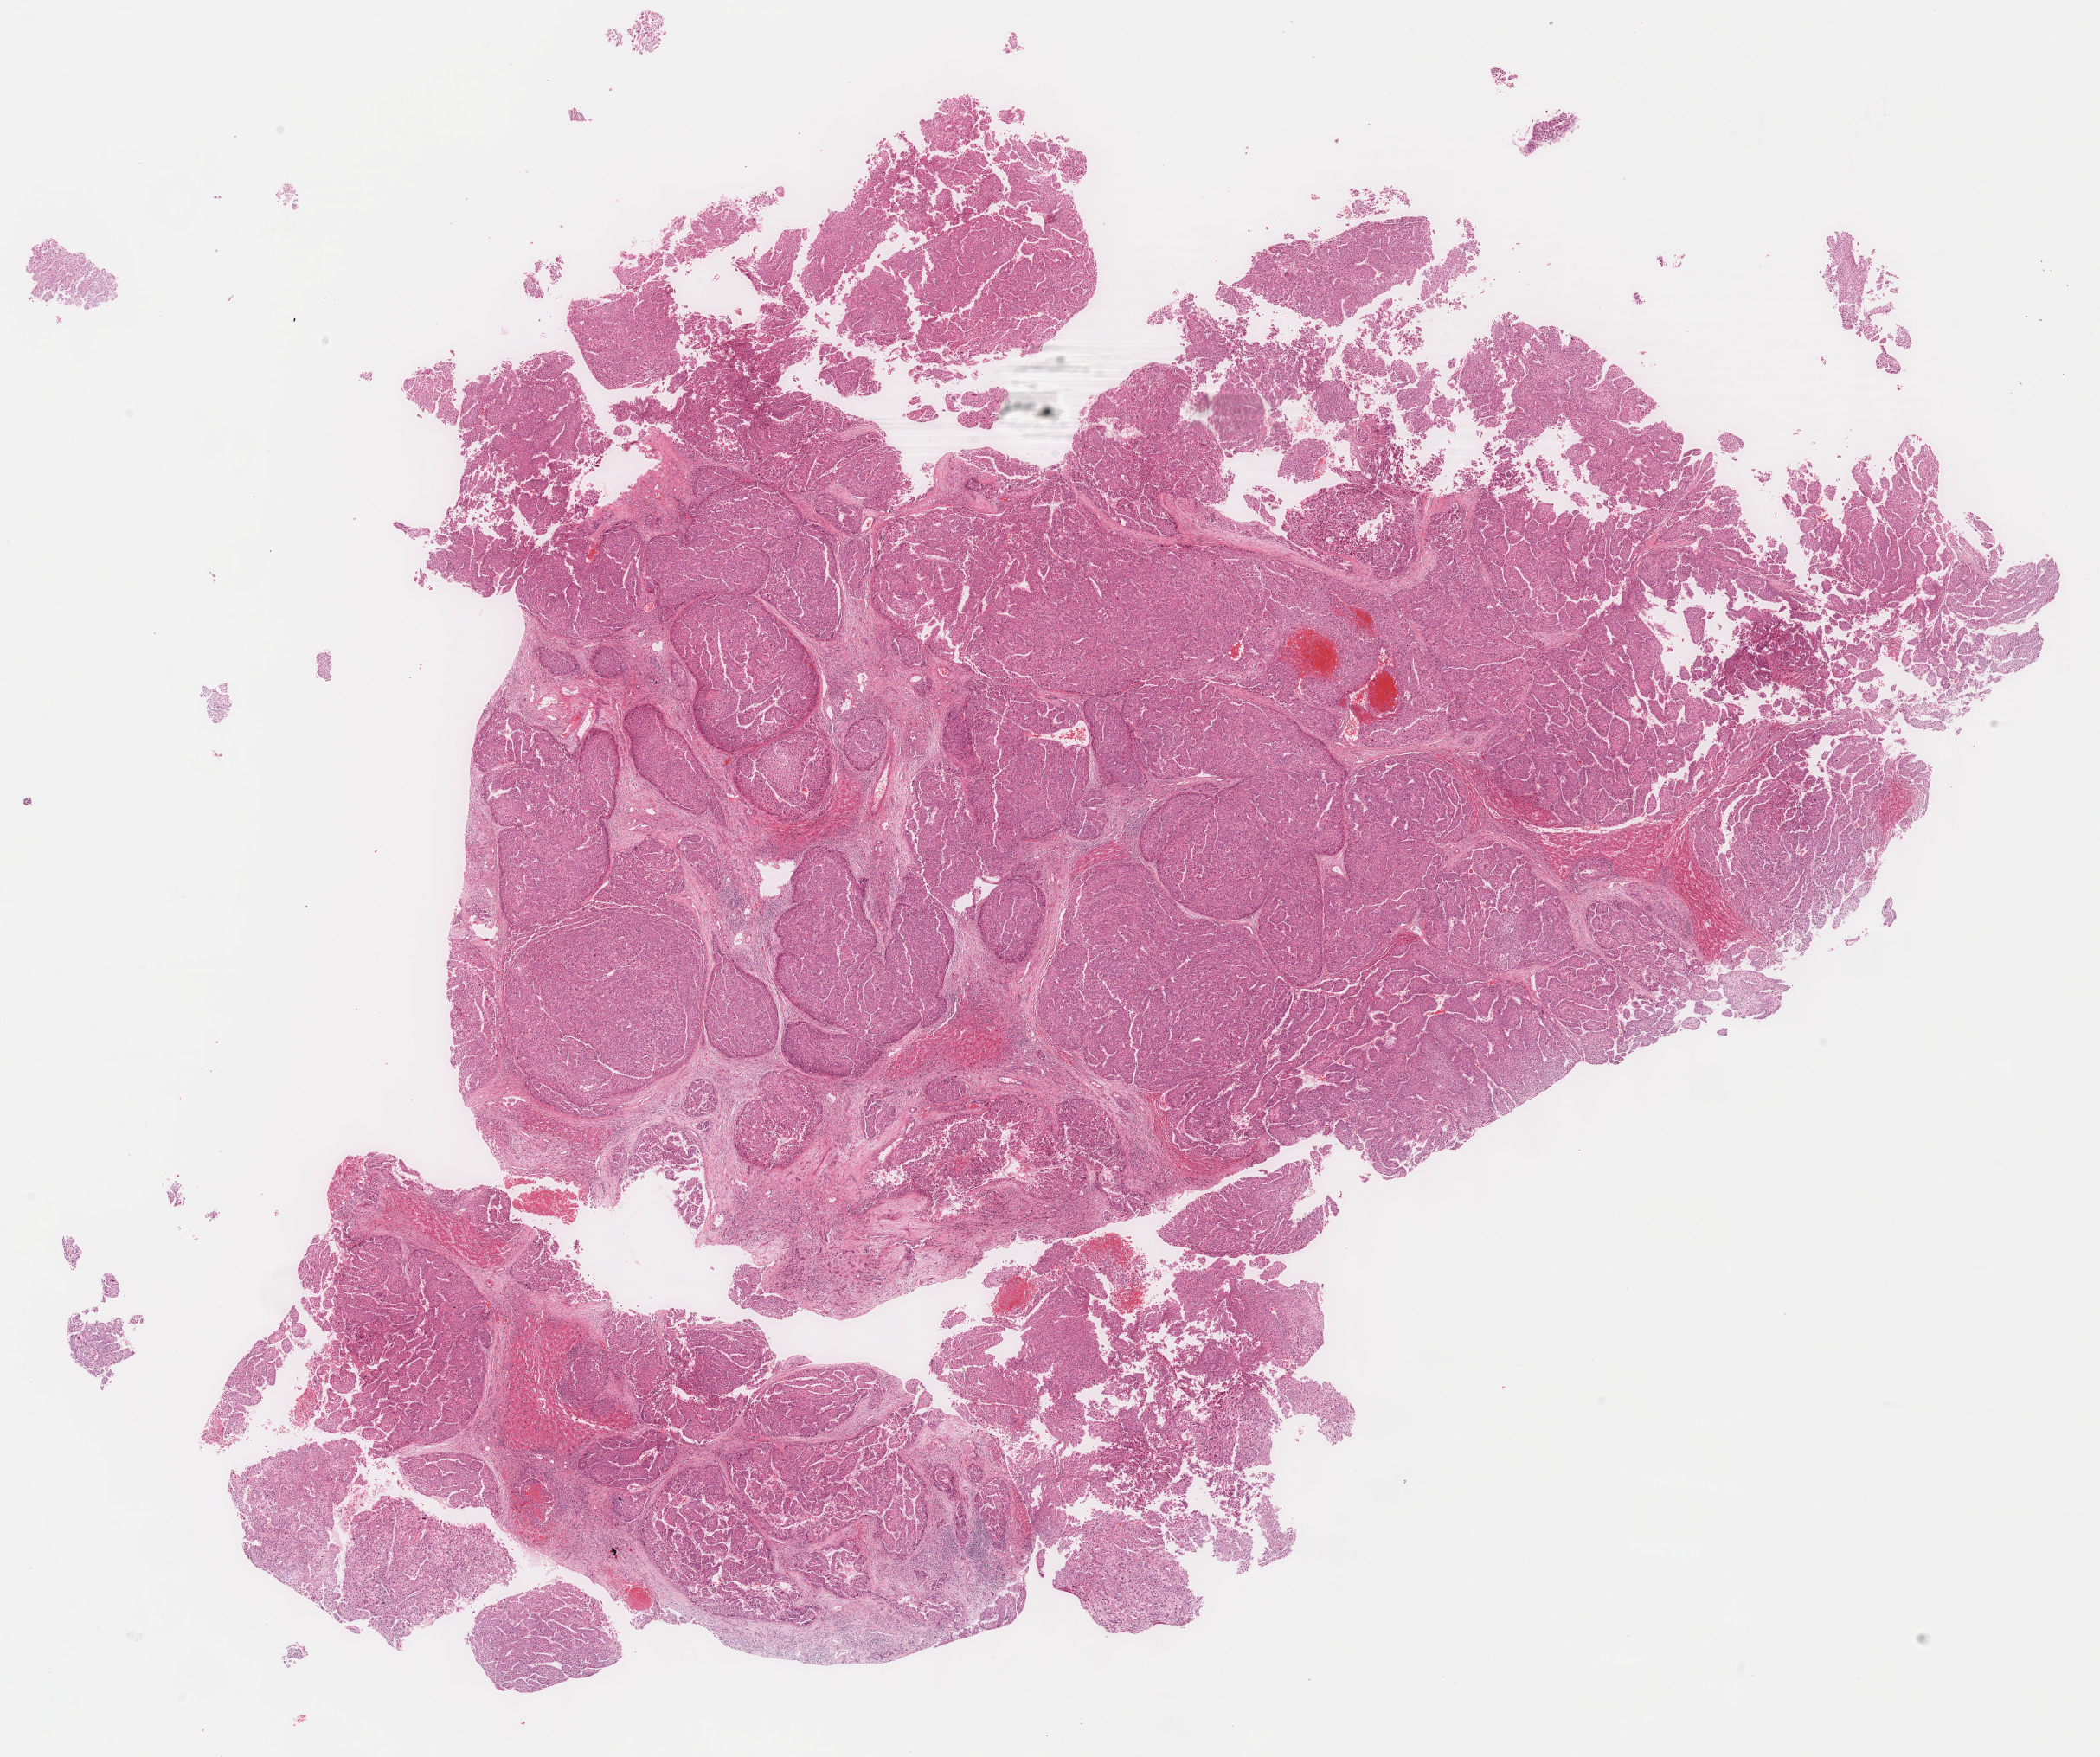
Whole-slide histology image, Hematoxylin and eosin (H&E) stained, whole scanned area (about 19.6 x 16.4 mm, slide scanned at 40x) shown as a low-resolution overview, formalin-fixed paraffin-embedded (FFPE) diagnostic section, sample: primary tumour, liver. Patient: male, age at initial diagnosis 53 years.
Pathologic diagnosis: Hepatocellular carcinoma, NOS.